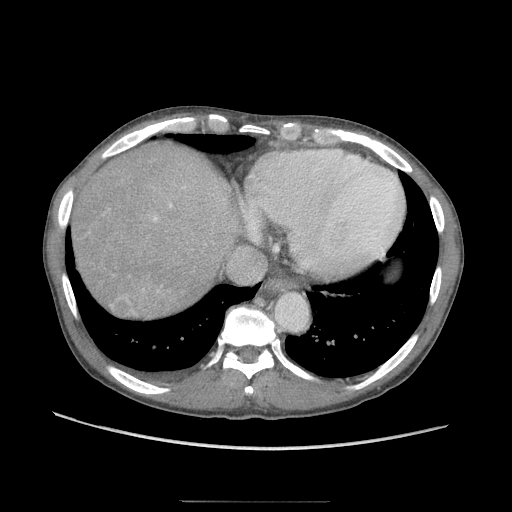
Contrast-enhanced abdominal CT (liver protocol), one axial slice. Slice 87 of 103 in the series (ordered by position). Reconstruction kernel STANDARD. Soft-tissue window (W 400 / L 40 HU). 2.5 mm slice thickness. 512 × 512 image matrix, field of view 380 × 380 mm. Case-level facts recorded for this patient, not image findings: diagnosis: hepatocellular carcinoma (patient treated with transarterial chemoembolisation; whether this scan precedes or follows treatment is not stated here); TNM stage (as recorded): Stage-IIIA; Child-Pugh class: A; tumour differentiation: moderately differentiated; tumour nodularity: multinodular.
Structures marked on this image (semi-automatic segmentation, software-assisted and operator-edited):
- abdominal aorta: box from (x=276, y=294) to (x=308, y=330) px
- liver parenchyma outside the tumour (the mass and vessels are separate outlines, so this box may not span the whole liver): (x=74, y=142)–(x=224, y=308)
- mass: (x=112, y=292)–(x=132, y=312)